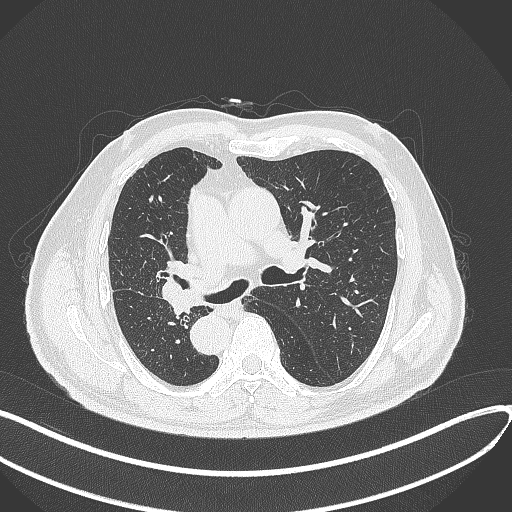
Chest CT, one axial slice; slice 176 of 300 in the series (ordered by position); reconstruction kernel B70f; 120 kVp; lung window (W 1500 / L -600 HU); 1 mm slice thickness; 512 × 512 image matrix. Male patient, age 67 years. Case-level facts recorded for this patient, not image findings: clinical TNM (as recorded): T2a N0 M0.
Outlined on this slice (rectangle marked by the reading radiologist):
- lung tumour (recorded histology: squamous cell carcinoma): bounding box (x1, y1, x2, y2) in pixels: (153, 261, 198, 310)